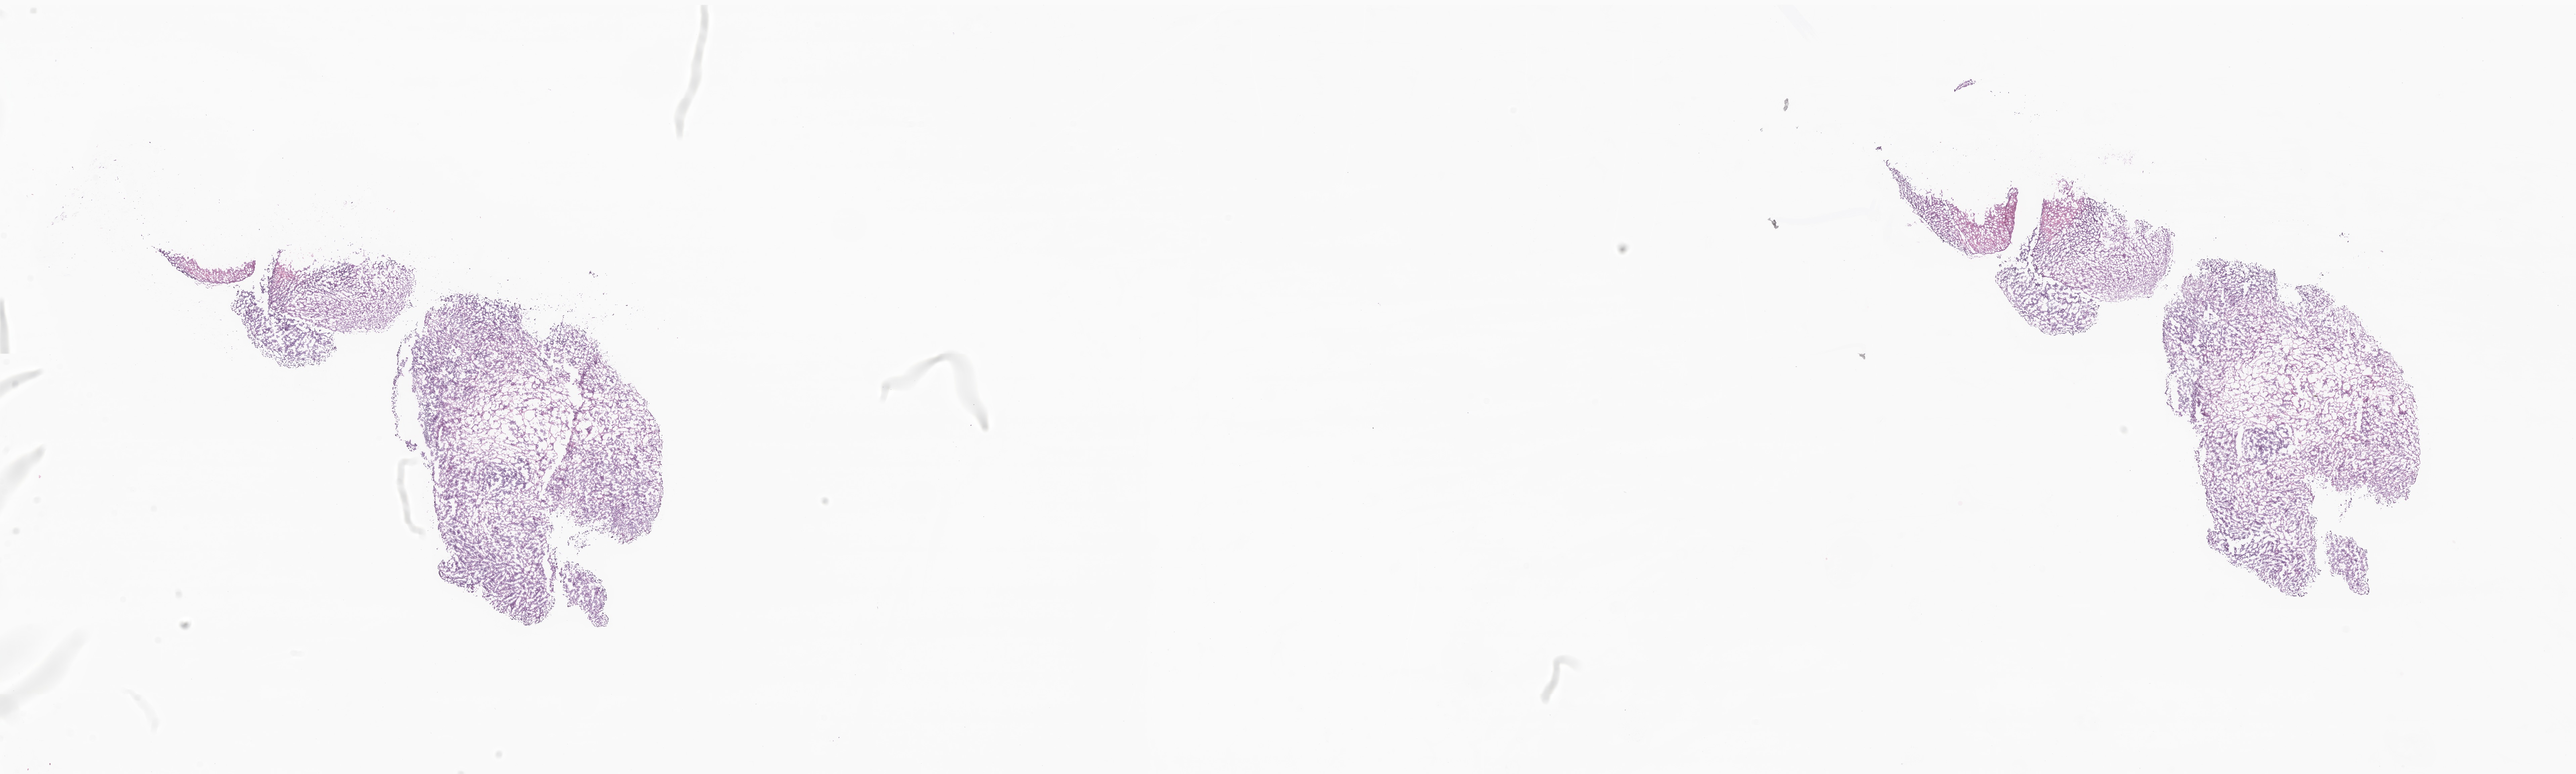
Whole-slide image, H&E stain of tumor tissue from the brain — whole scanned area (about 32.3 x 9.7 mm) shown as a low-resolution overview, cryosection (OCT / tissue freezing medium). Male patient, age 63 months (5 years 3 months).
Diagnosis: Medulloblastoma, NOS.